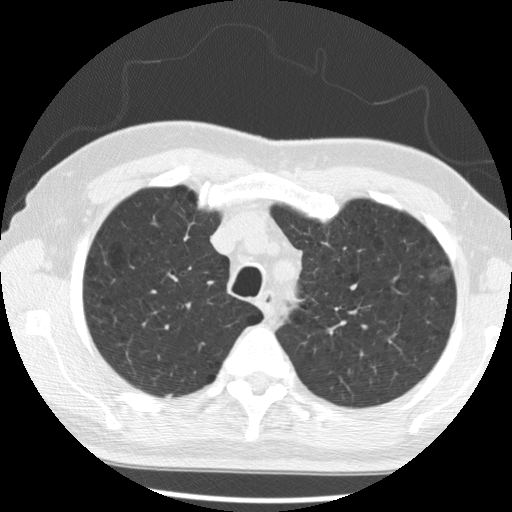
Axial slice from a low-dose chest CT screening exam, second screening round (one year after baseline), lung window (W 1500 / L -600 HU), standard (soft-tissue) reconstruction kernel (STANDARD), 120 kVp, slice 63 of 285 in the series. Male participant, aged 68 years at enrolment.
• Expert reader's lesion annotation, bounding box <417,260,461,294> (left, top, right, bottom; pixels).
• Screening reader's record for this exam (one nodule recorded; not confirmed to be the boxed lesion): non-calcified nodule or mass ≥4 mm, left upper lobe, 15 × 11 mm, poorly defined margins, ground glass attenuation, pre-existing on the prior screen: yes; interval growth: yes.
• Official screen result: positive, change unspecified: nodule(s) >= 4 mm or enlarging nodule(s), mass(es), or other non-specific abnormalities suspicious for lung cancer.
• Participant outcome: lung cancer diagnosed 278 days after this screen — bronchiolo-alveolar adenocarcinoma, NOS, left upper lobe, moderately differentiated (G2), stage IA (AJCC 6th edition), 17 mm at pathology.